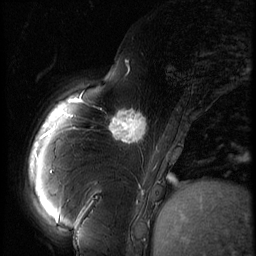
Breast MRI (dynamic contrast-enhanced), one sagittal slice; 3 images stored at this slice position (order not interpretable as contrast timing); 1.5 T; TE 4.2 ms, TR 9 ms; 2.5 mm slice thickness; 256 × 256 image matrix, field of view 180 × 180 mm. Female patient, age 57 years. From the clinical record (not read from this slice): setting: breast cancer imaged before/during neoadjuvant chemotherapy; receptor status: triple-negative.
Outlined on this slice (semi-automatic segmentation, software-assisted and operator-edited):
- analysis volume of interest (the breast-tissue region the enhancement analysis was run in; not a lesion): bounding box <106,101,157,152> (left, top, right, bottom; pixels)
- tumour enhancement mask (voxels above the 140 % enhancement threshold inside the analysis volume of interest): <109,110,146,144>